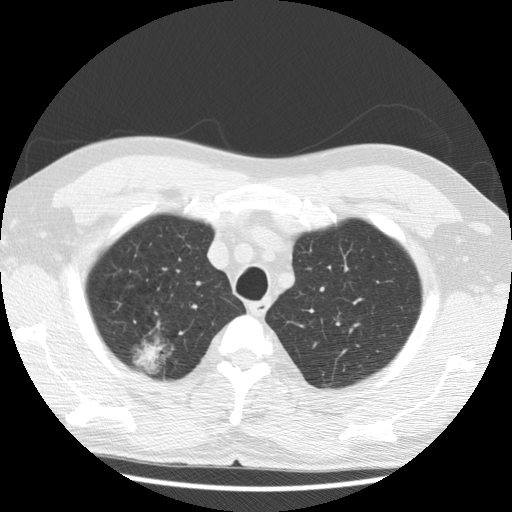
Axial slice from a low-dose chest CT screening exam. Baseline annual screen. Lung window (W 1500 / L -600 HU). Standard (soft-tissue) reconstruction kernel (STANDARD). 512 × 512 image matrix, field of view 350 × 350 mm. Male participant, aged 59 years at enrolment. Former smoker at enrolment.
Expert reader's lesion annotation, box from (x=121, y=327) to (x=181, y=384) px. Screening reader's record for this exam (one nodule recorded; not confirmed to be the boxed lesion): non-calcified nodule or mass ≥4 mm, right upper lobe, 30 × 28 mm, poorly defined margins, ground glass attenuation. Official screen result: positive, change unspecified: nodule(s) >= 4 mm or enlarging nodule(s), mass(es), or other non-specific abnormalities suspicious for lung cancer. Later outcome: lung cancer diagnosed 40 days after this screen — bronchiolo-alveolar carcinoma, non-mucinous, right upper lobe, well differentiated (G1), stage IA (AJCC 6th edition), 15 mm at pathology.